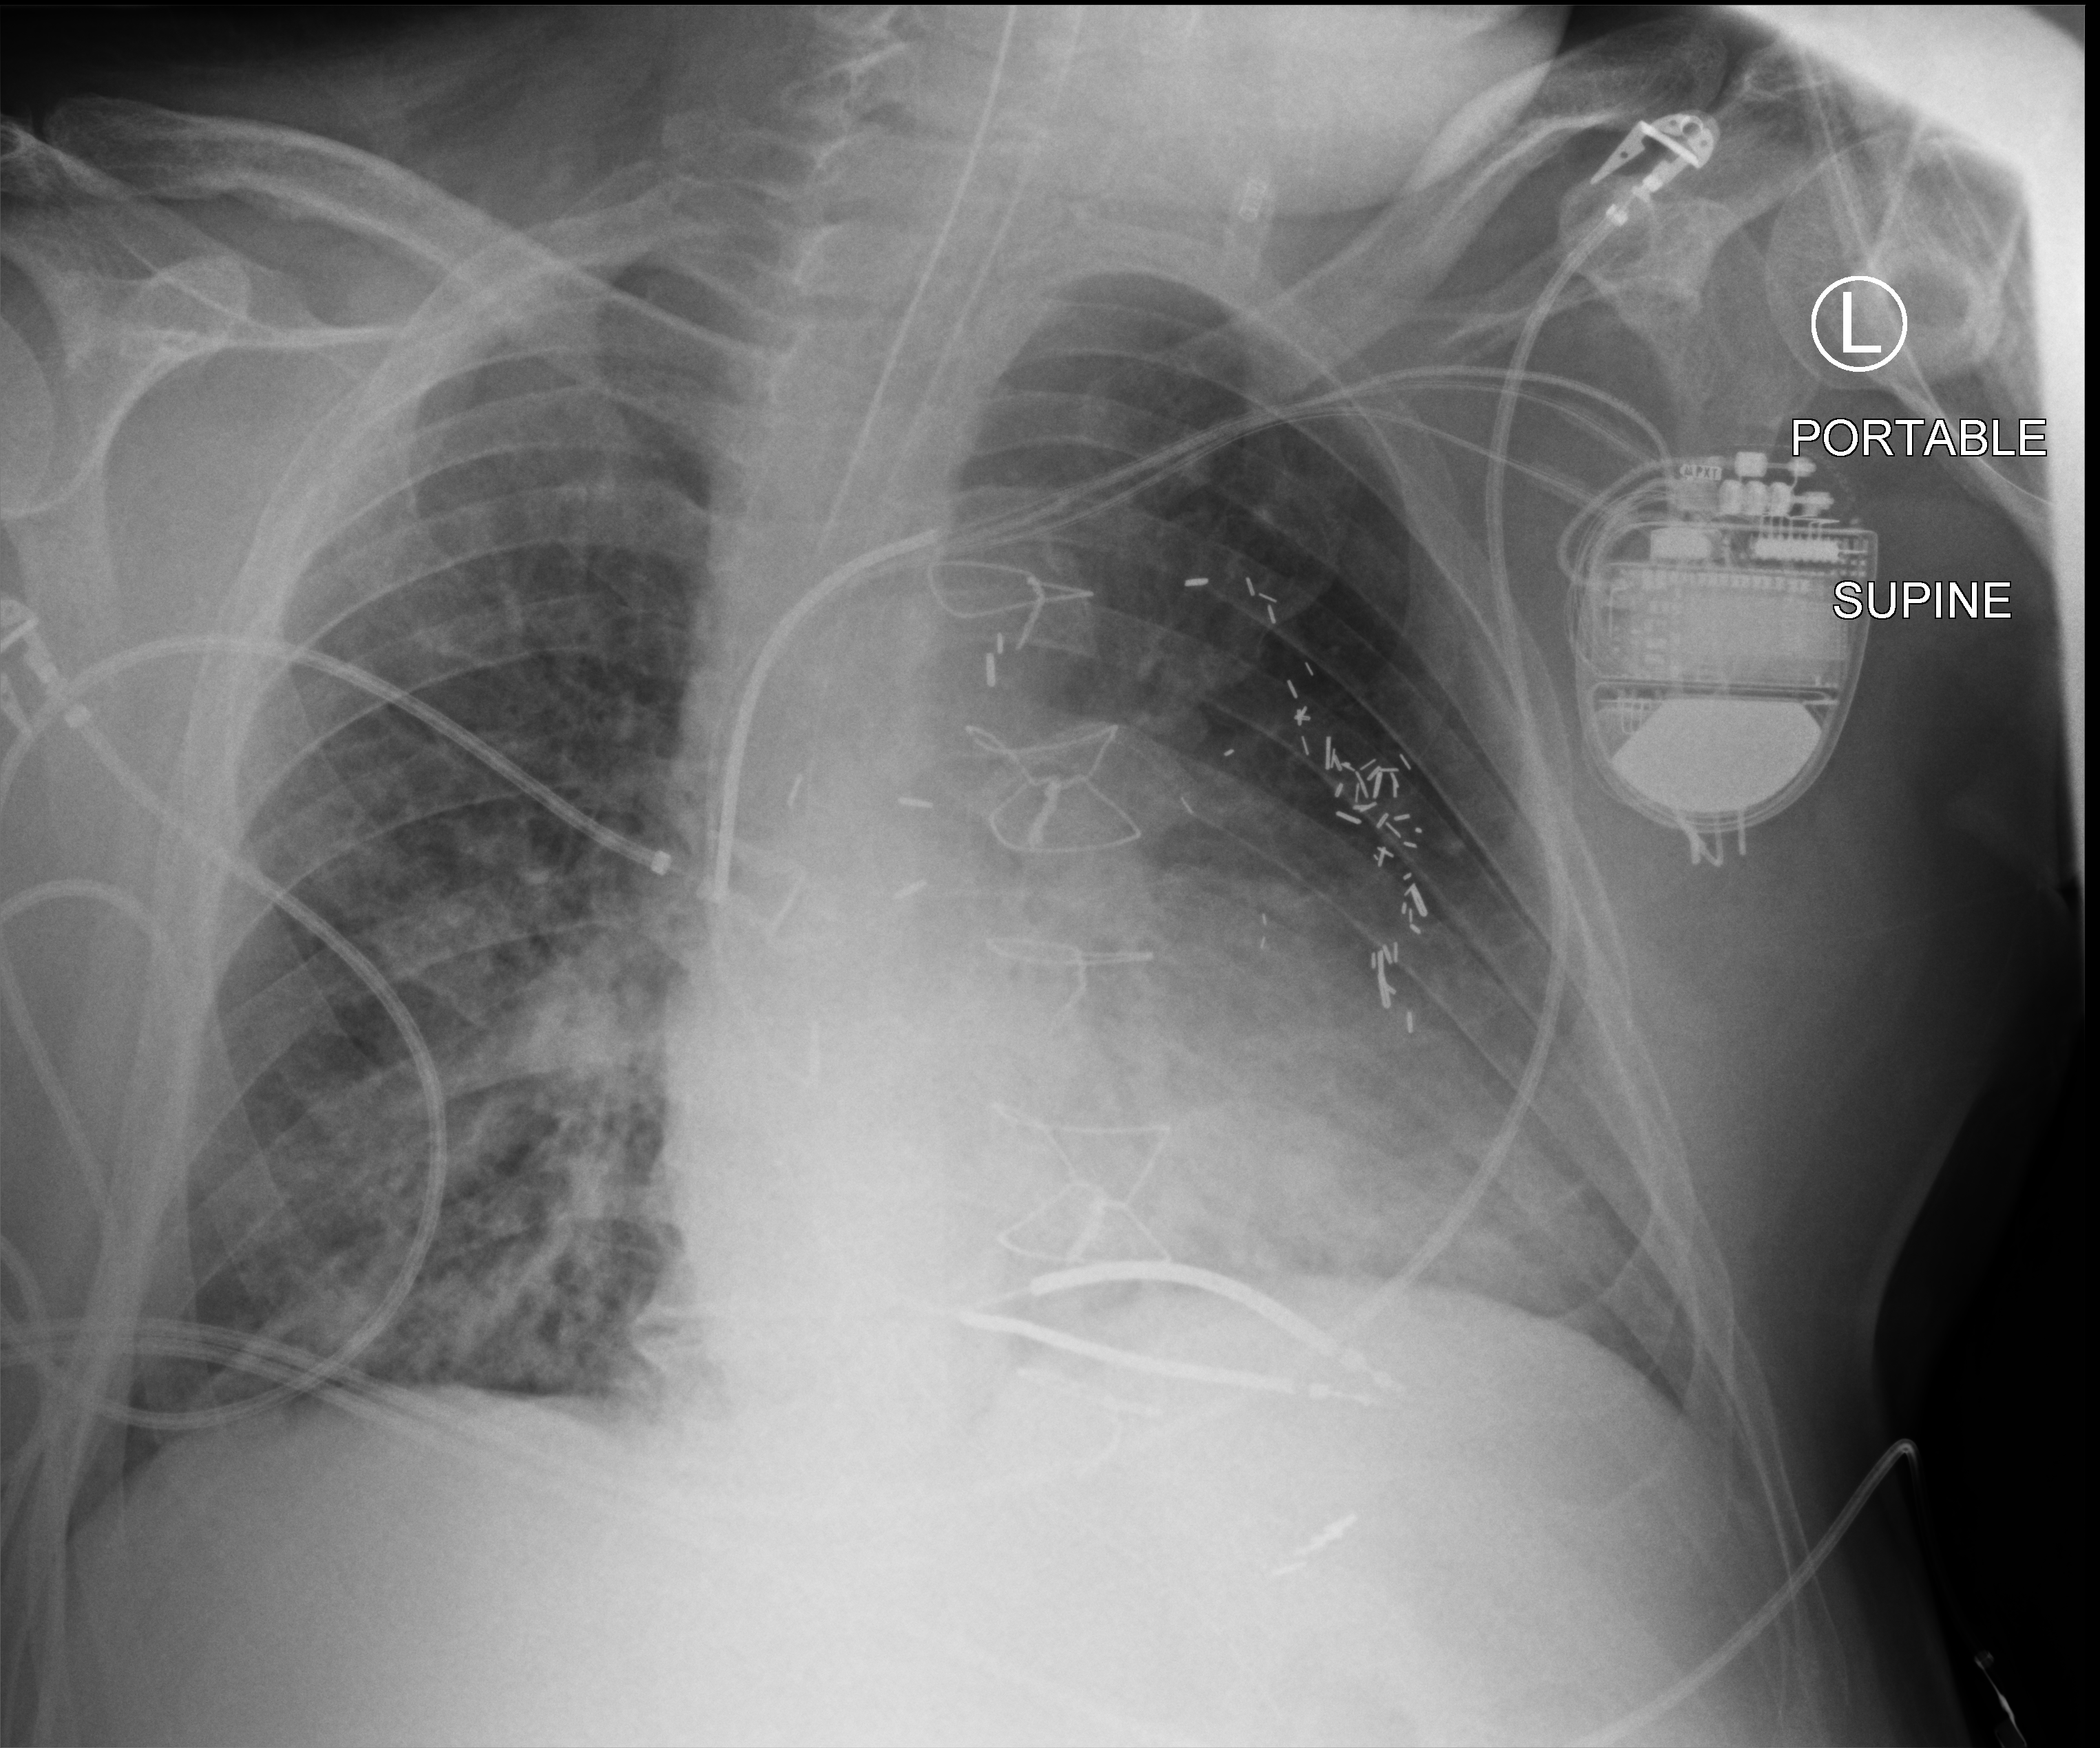
Bedside chest radiograph (computed radiography), anteroposterior (AP) projection. Patient hospitalised with COVID-19; male, aged 60–74 years.
Hospital-stay facts (about this admission, not read from this image; timing relative to this image not recorded): diabetes (admission record): yes.